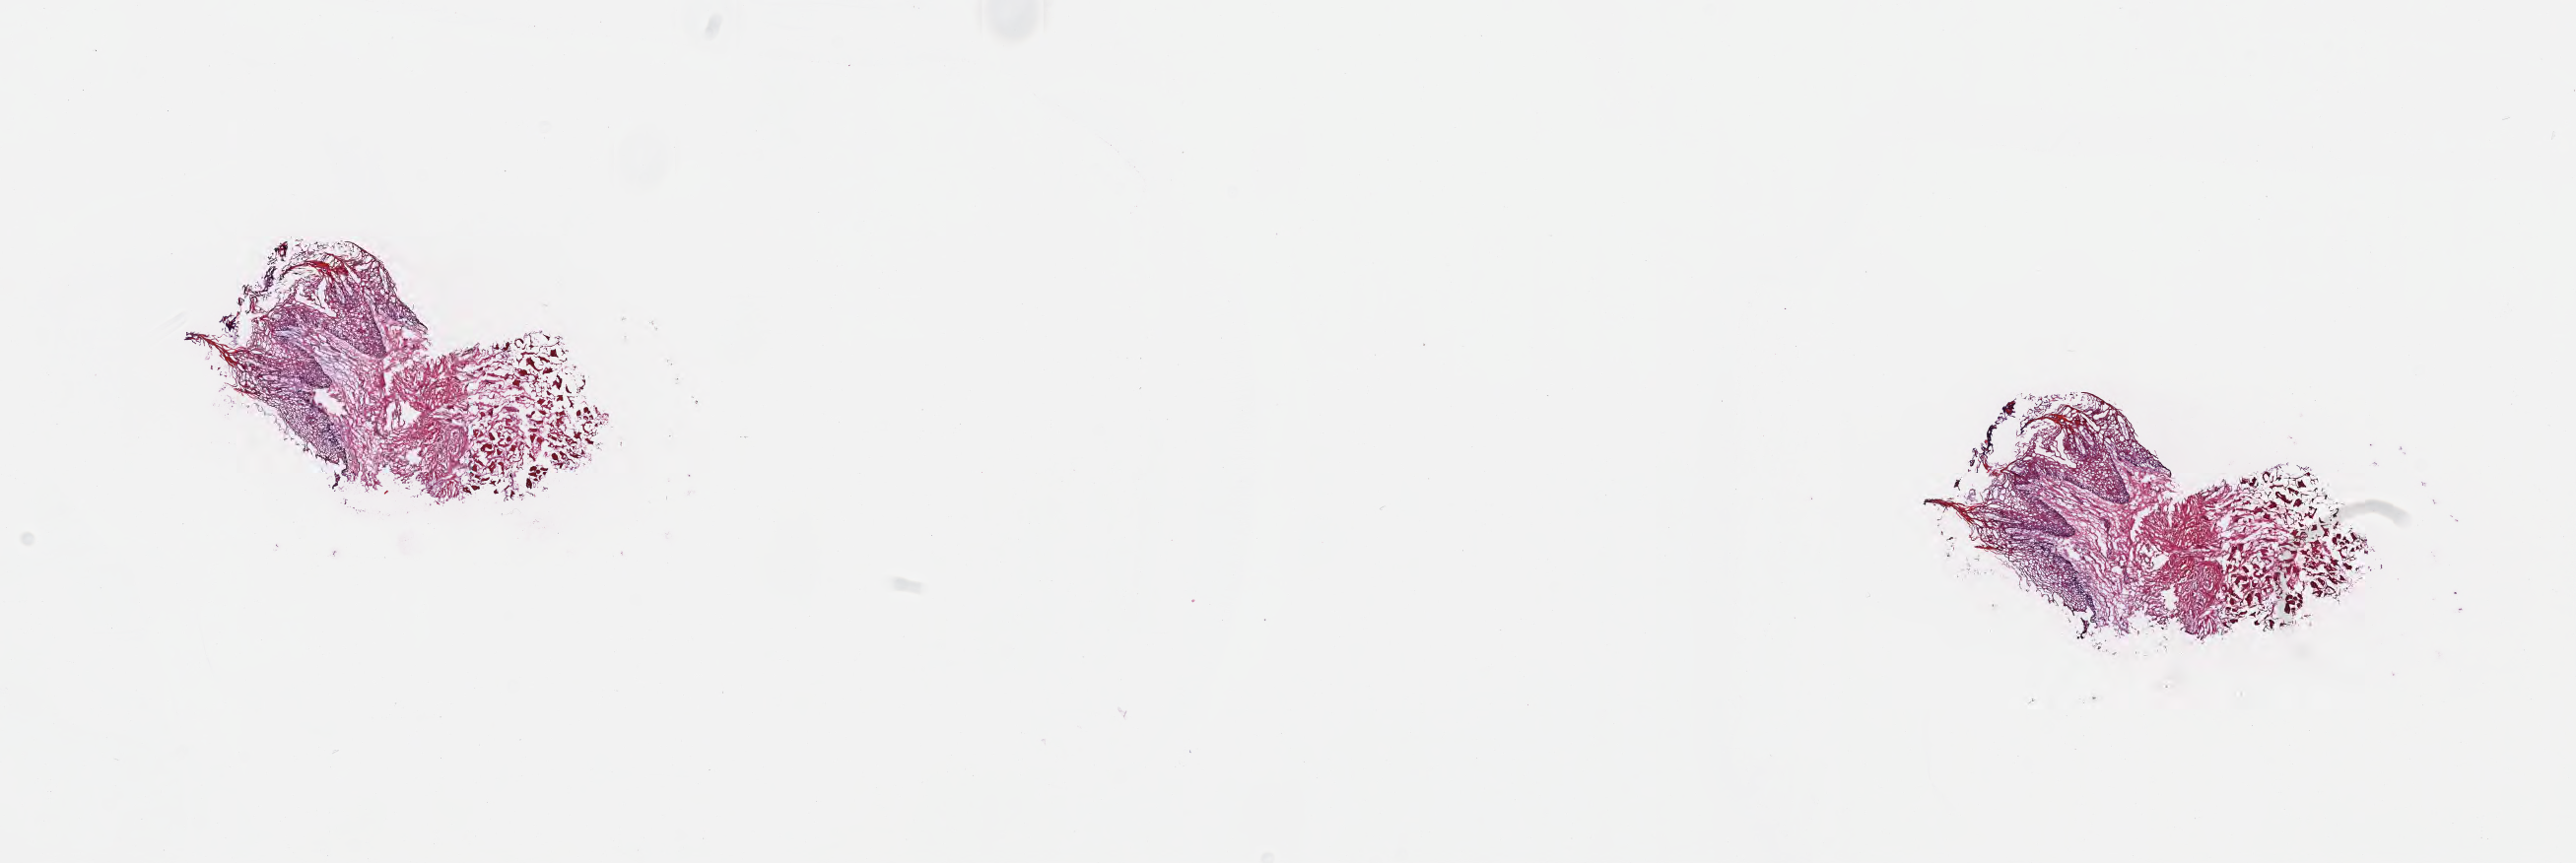
Whole-slide image, H&E stain — a low-resolution overview of the entire scanned area, about 21.1 x 7.1 mm, cryosection, non-tumor (normal tissue) sample from a patient with squamous cell carcinoma, NOS, site: border of tongue (left). Patient sex: male. Composition of this section per pathologist review: tumor cells 0%, tumor nuclei 0%, stromal cells 0%, necrosis 0%, normal cells 100%. Inflammatory infiltration, as recorded: lymphocyte infiltration 0%, monocyte infiltration 0%, neutrophil infiltration 0%.
This section: non-tumor tissue sample; the patient's diagnosis is given above. Section: top of the tissue portion.